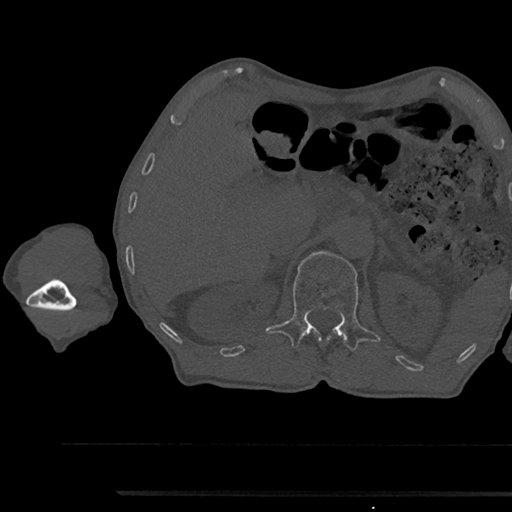
CT including the spine, one axial slice; position 655 of 797 along the scan axis; reconstruction kernel Br40s/3; 120 kVp; bone window (W 1800 / L 400 HU); 0.5 mm slice thickness; 512 × 512 image matrix, field of view 367 × 367 mm. Patient: male, 79 years. From the clinical record (not read from this slice): primary cancer: prostate.
Outlined on this slice (semi-automatically segmented with operator editing):
- L1 vertebra: bounding box <266,251,381,350> (left, top, right, bottom; pixels)